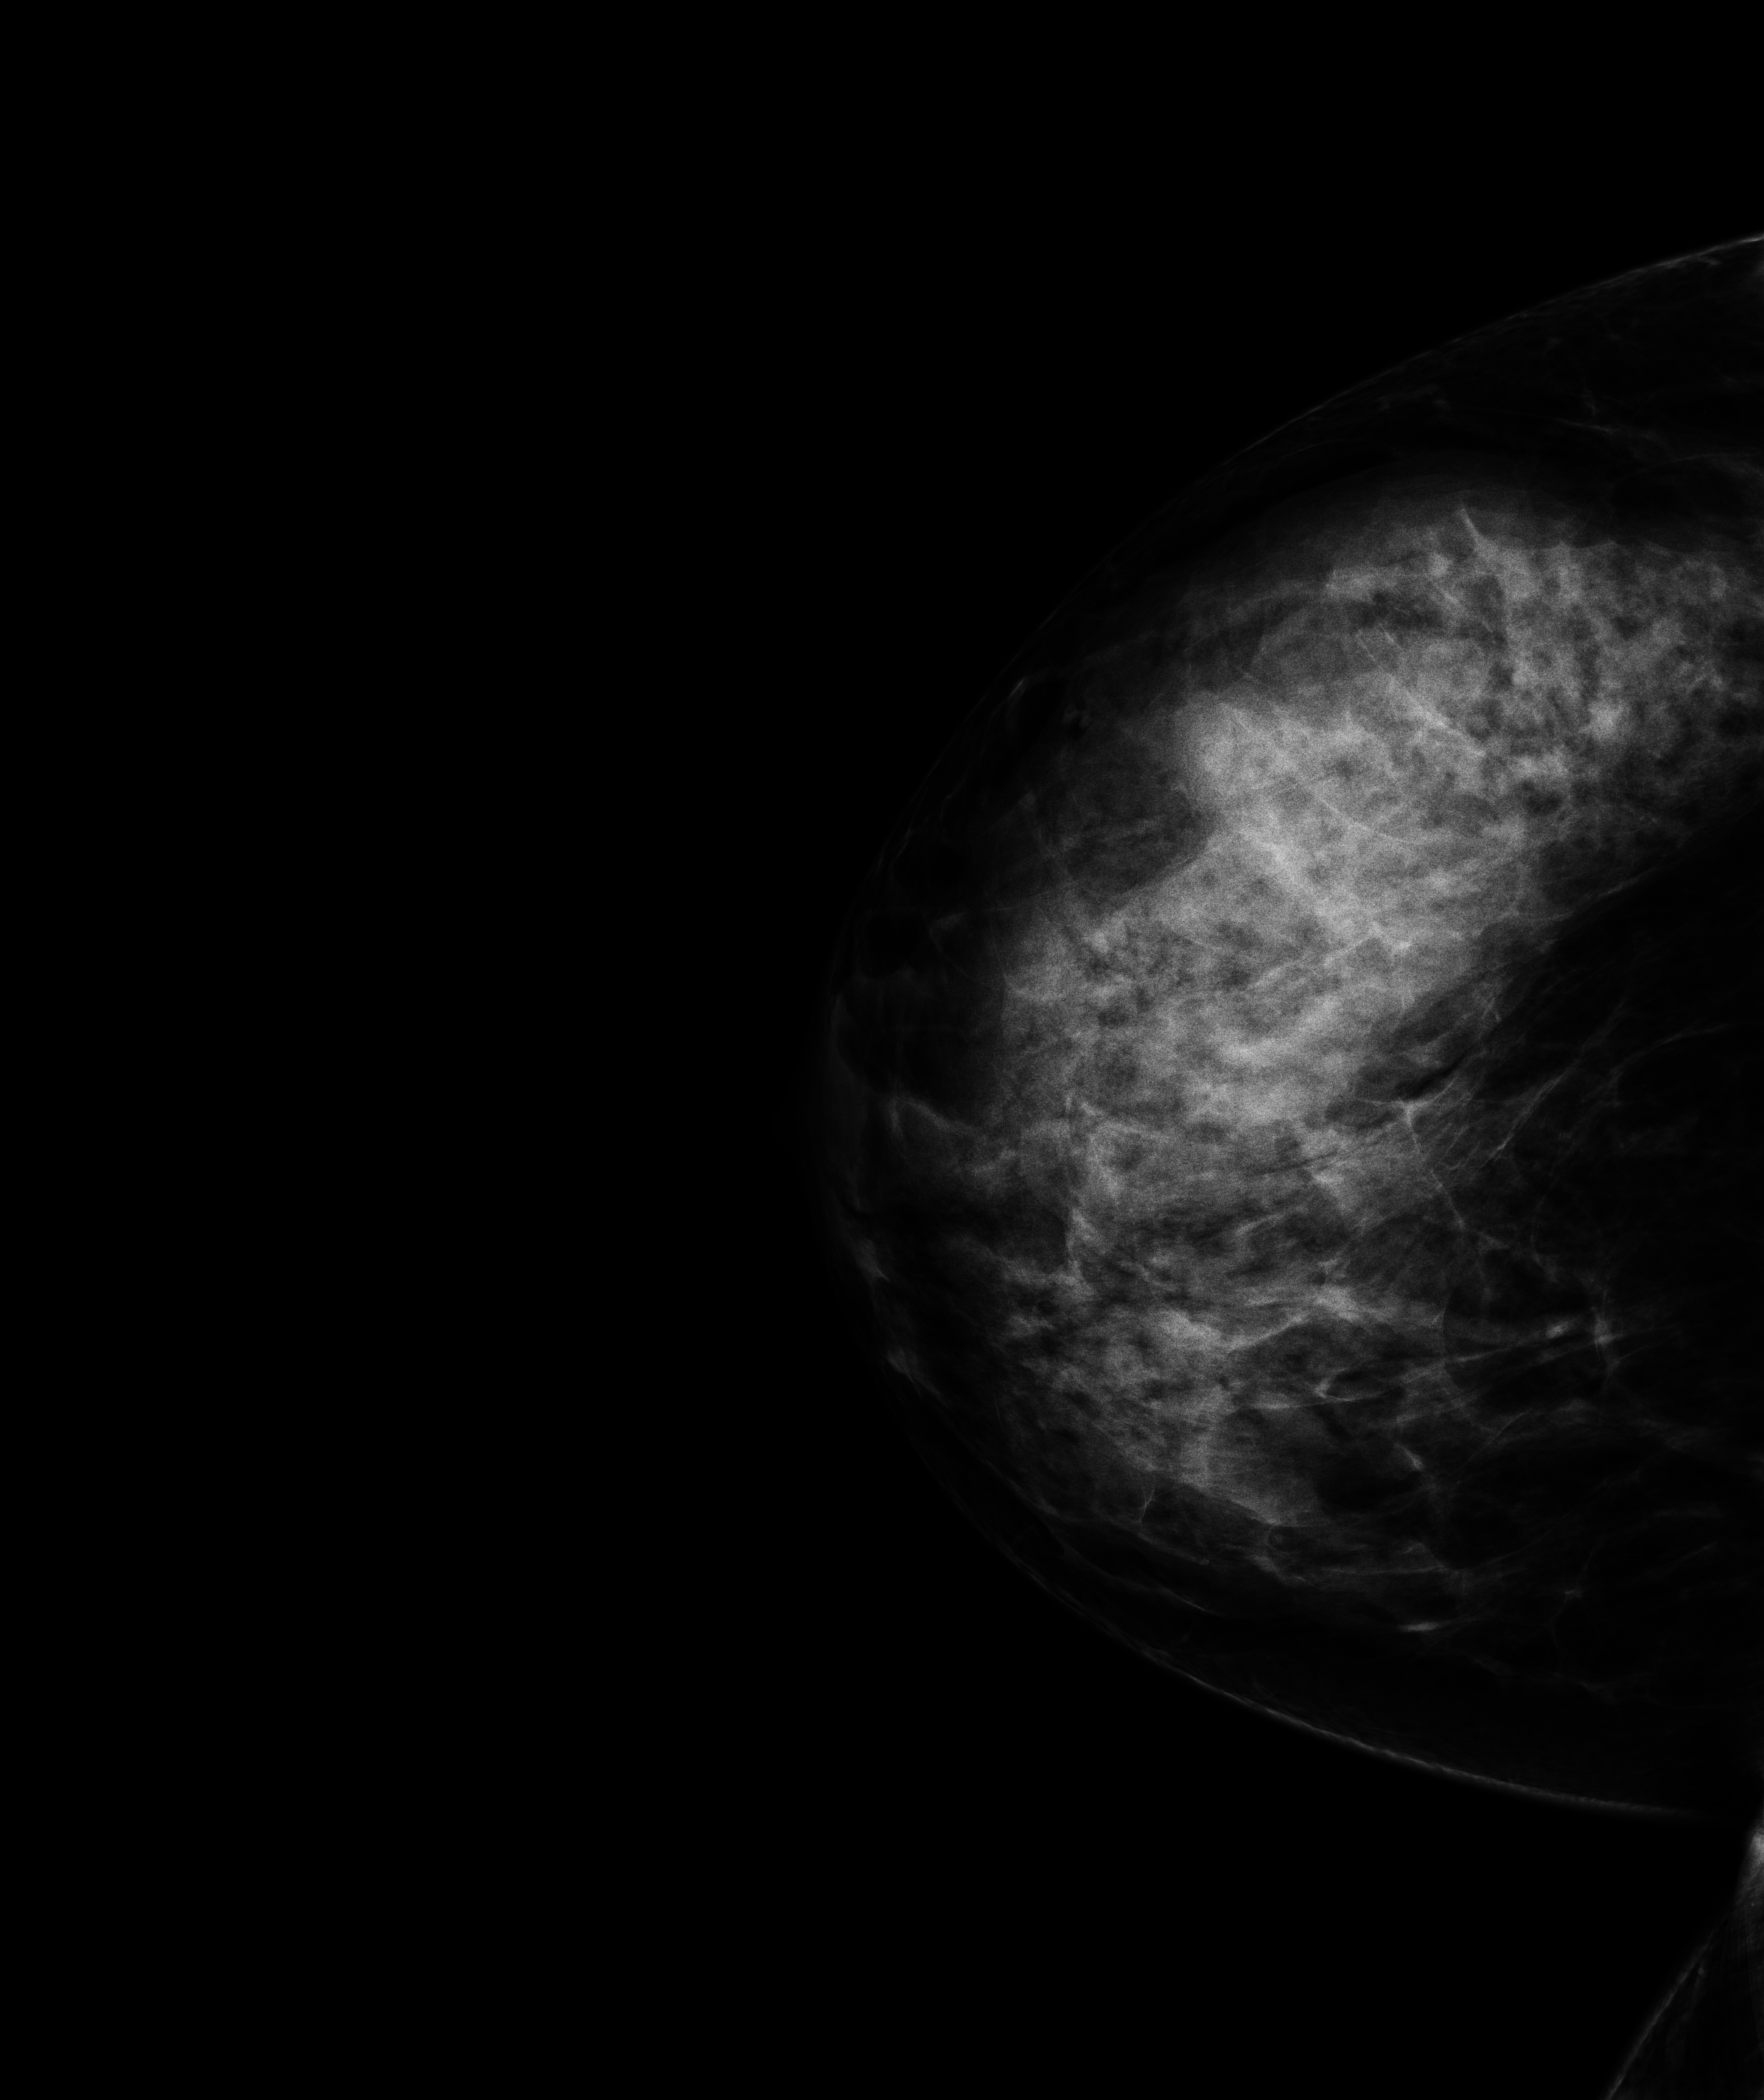
Annual screening mammography examination; compressed breast thickness 67.9 mm. Patient: female, 44 years.
Image type: full-field digital mammogram. Breast: right. Projection: CC view.